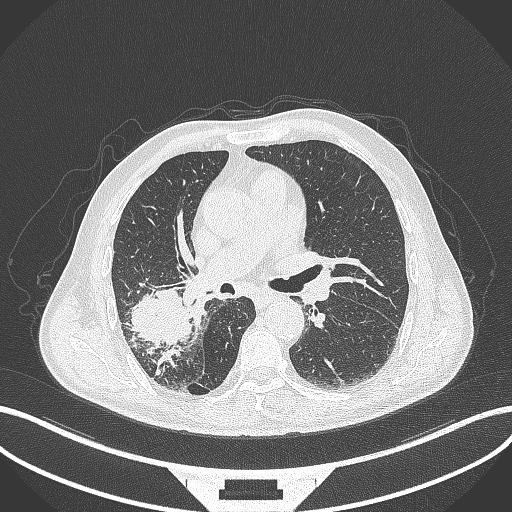
Chest CT, one axial slice; position 234 of 429 along the scan axis; reconstruction kernel B70f; lung window (W 1500 / L -600 HU); 512 × 512 image matrix, field of view 400 × 400 mm. Male patient, age 72 years. Case-level facts recorded for this patient, not image findings: clinical TNM (as recorded): T3 N2 M0.
Outlined on this slice (rectangle marked by the reading radiologist):
- lung tumour (recorded histology: adenocarcinoma): bounding box [x1, y1, x2, y2] px = [125, 283, 198, 353]